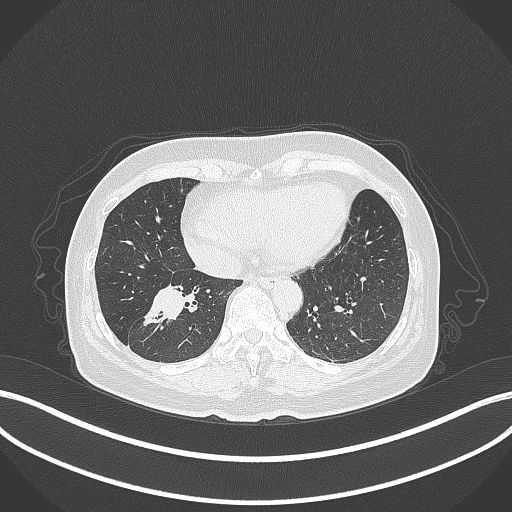
Chest CT, one axial slice. Slice 127 of 429 in the series (ordered by position). 120 kVp. Lung window (W 1500 / L -600 HU). 1 mm slice thickness. 512 × 512 image matrix, field of view 400 × 400 mm. Female patient, age 67 years. From the clinical record (not read from this slice): clinical TNM (as recorded): T1c N1 M0; histopathological grade: G2-3.
Structures marked on this image (bounding box drawn by a radiologist):
- lung tumour (recorded histology: adenocarcinoma): bounding box <143,279,196,326> (left, top, right, bottom; pixels)